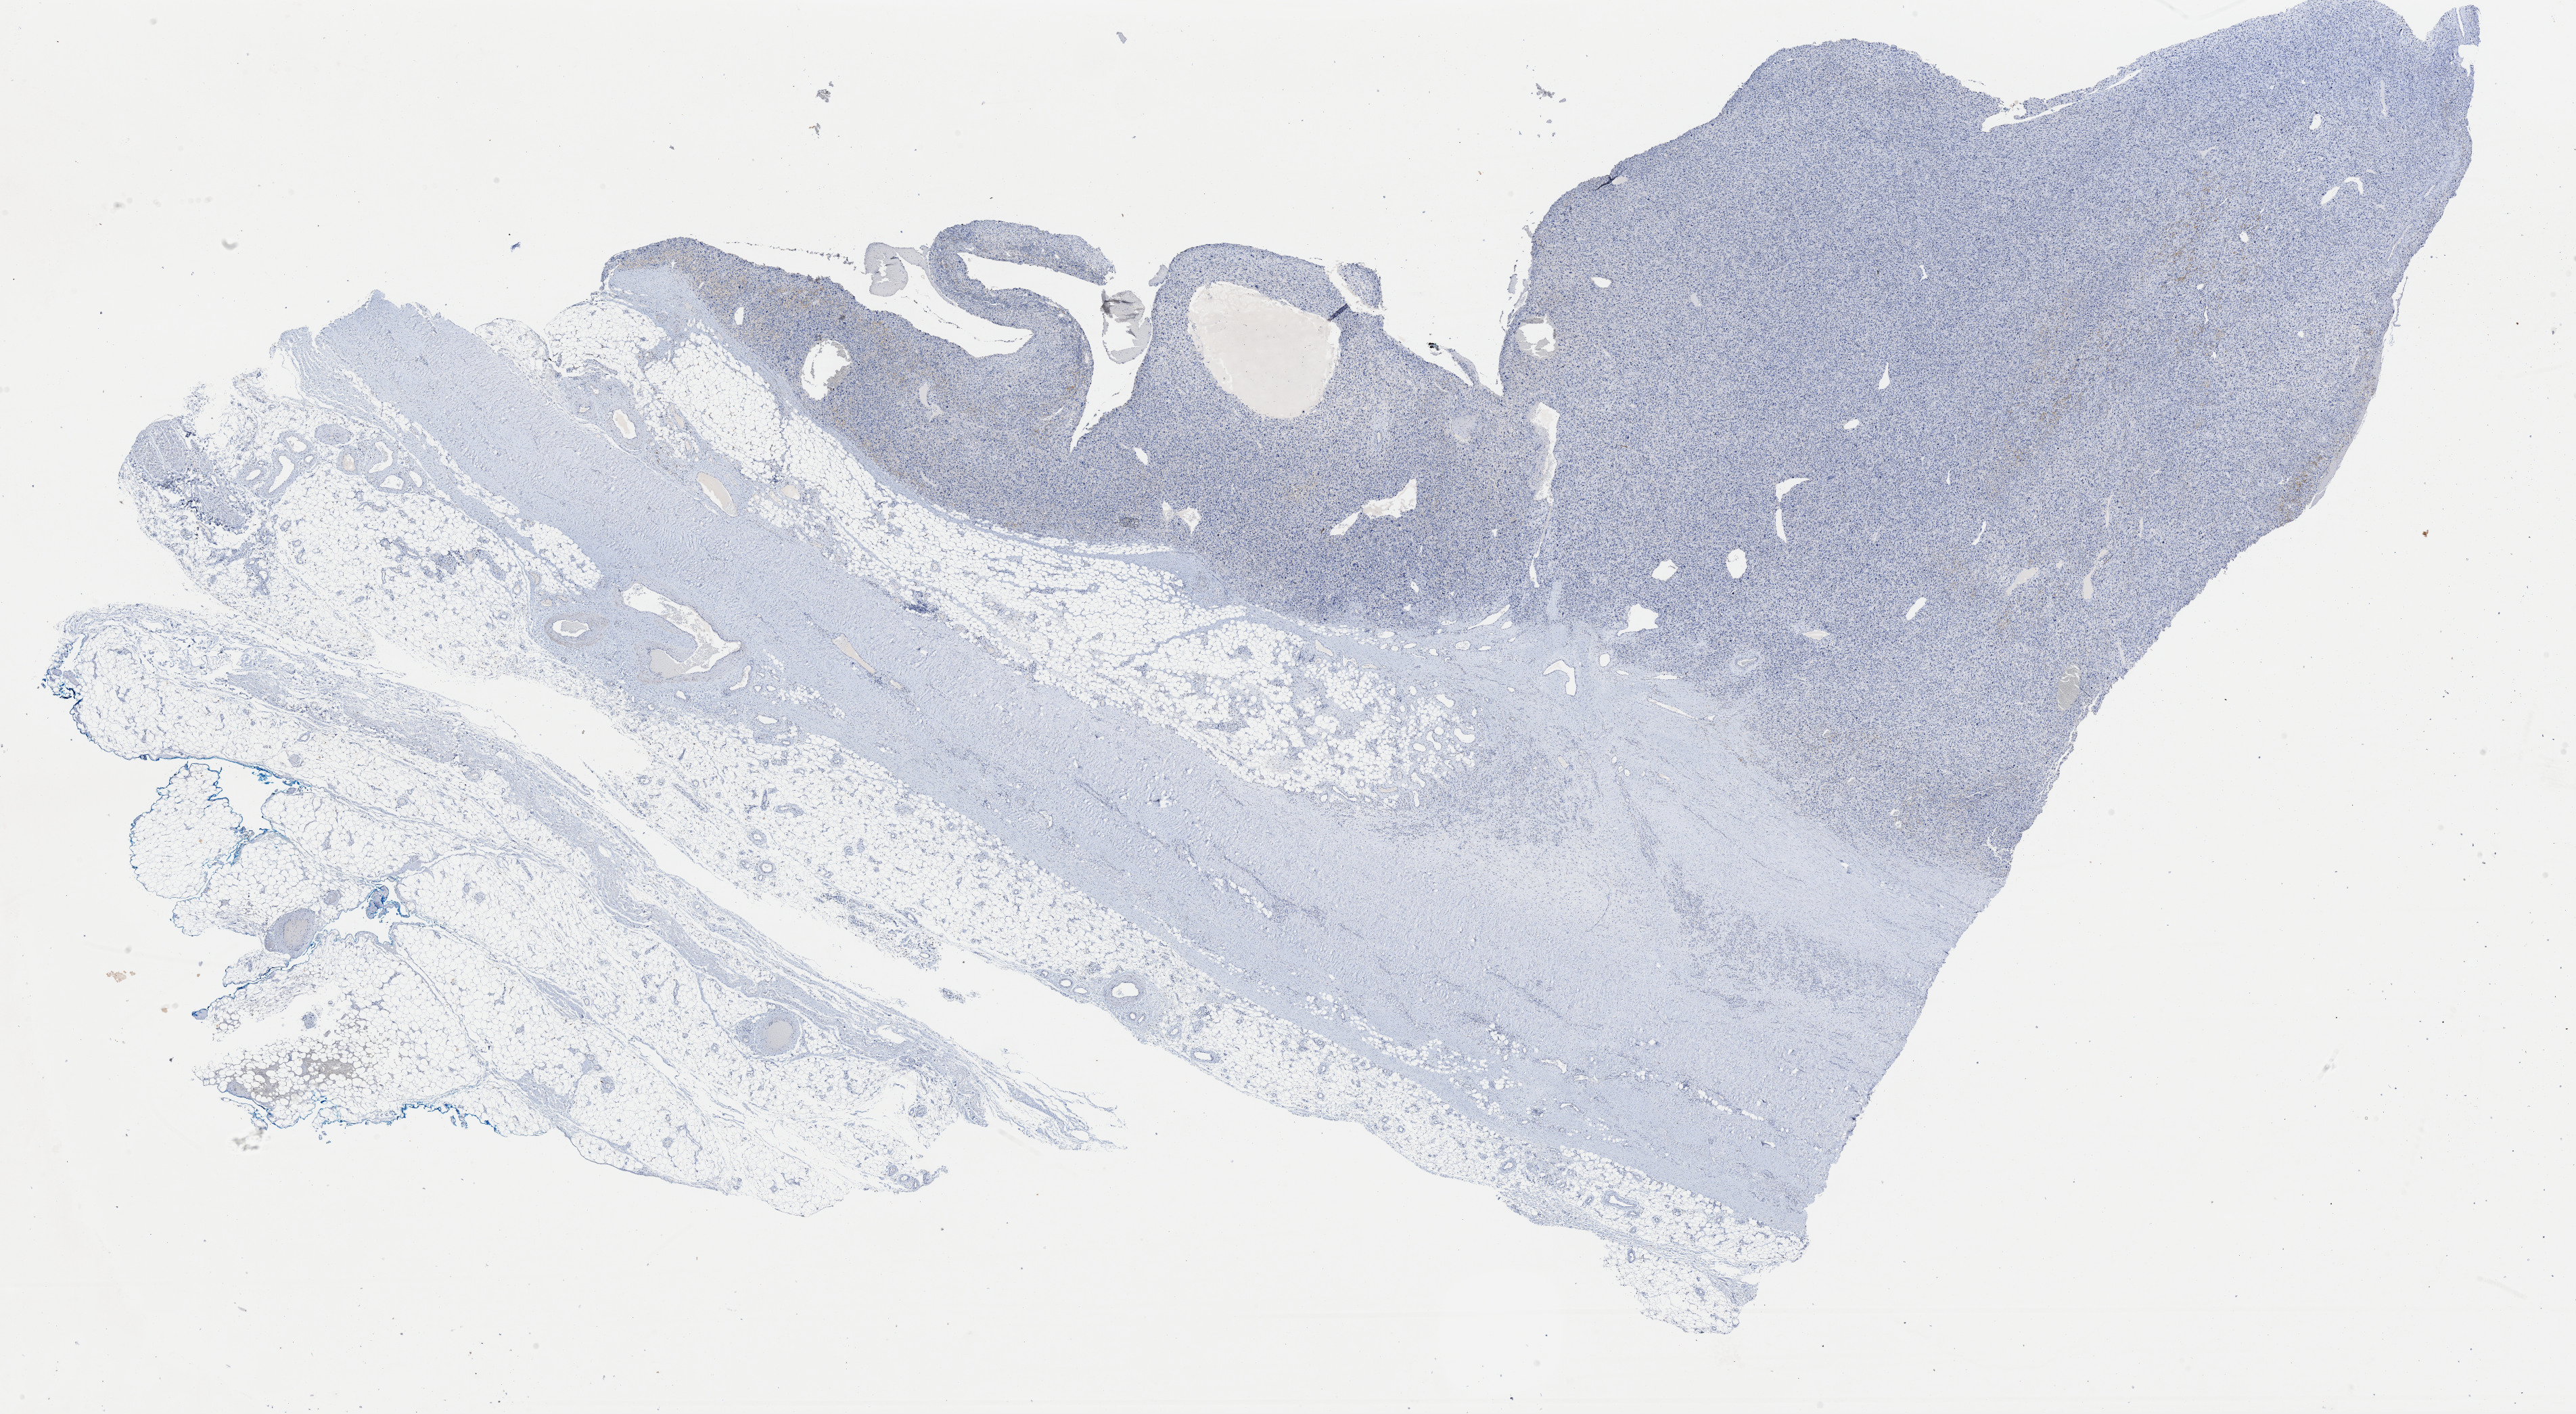
Digitized H&E-stained tissue section (whole slide) — shown as a low-resolution overview of the whole scanned area (about 30.1 x 16.5 mm, from a 40x scan). Formalin-fixed paraffin-embedded (FFPE) diagnostic section. Sample: primary tumour, connective, subcutaneous and other soft tissues. Patient: female, age at initial diagnosis 75 years.
Pathologic diagnosis: Malignant fibrous histiocytoma.